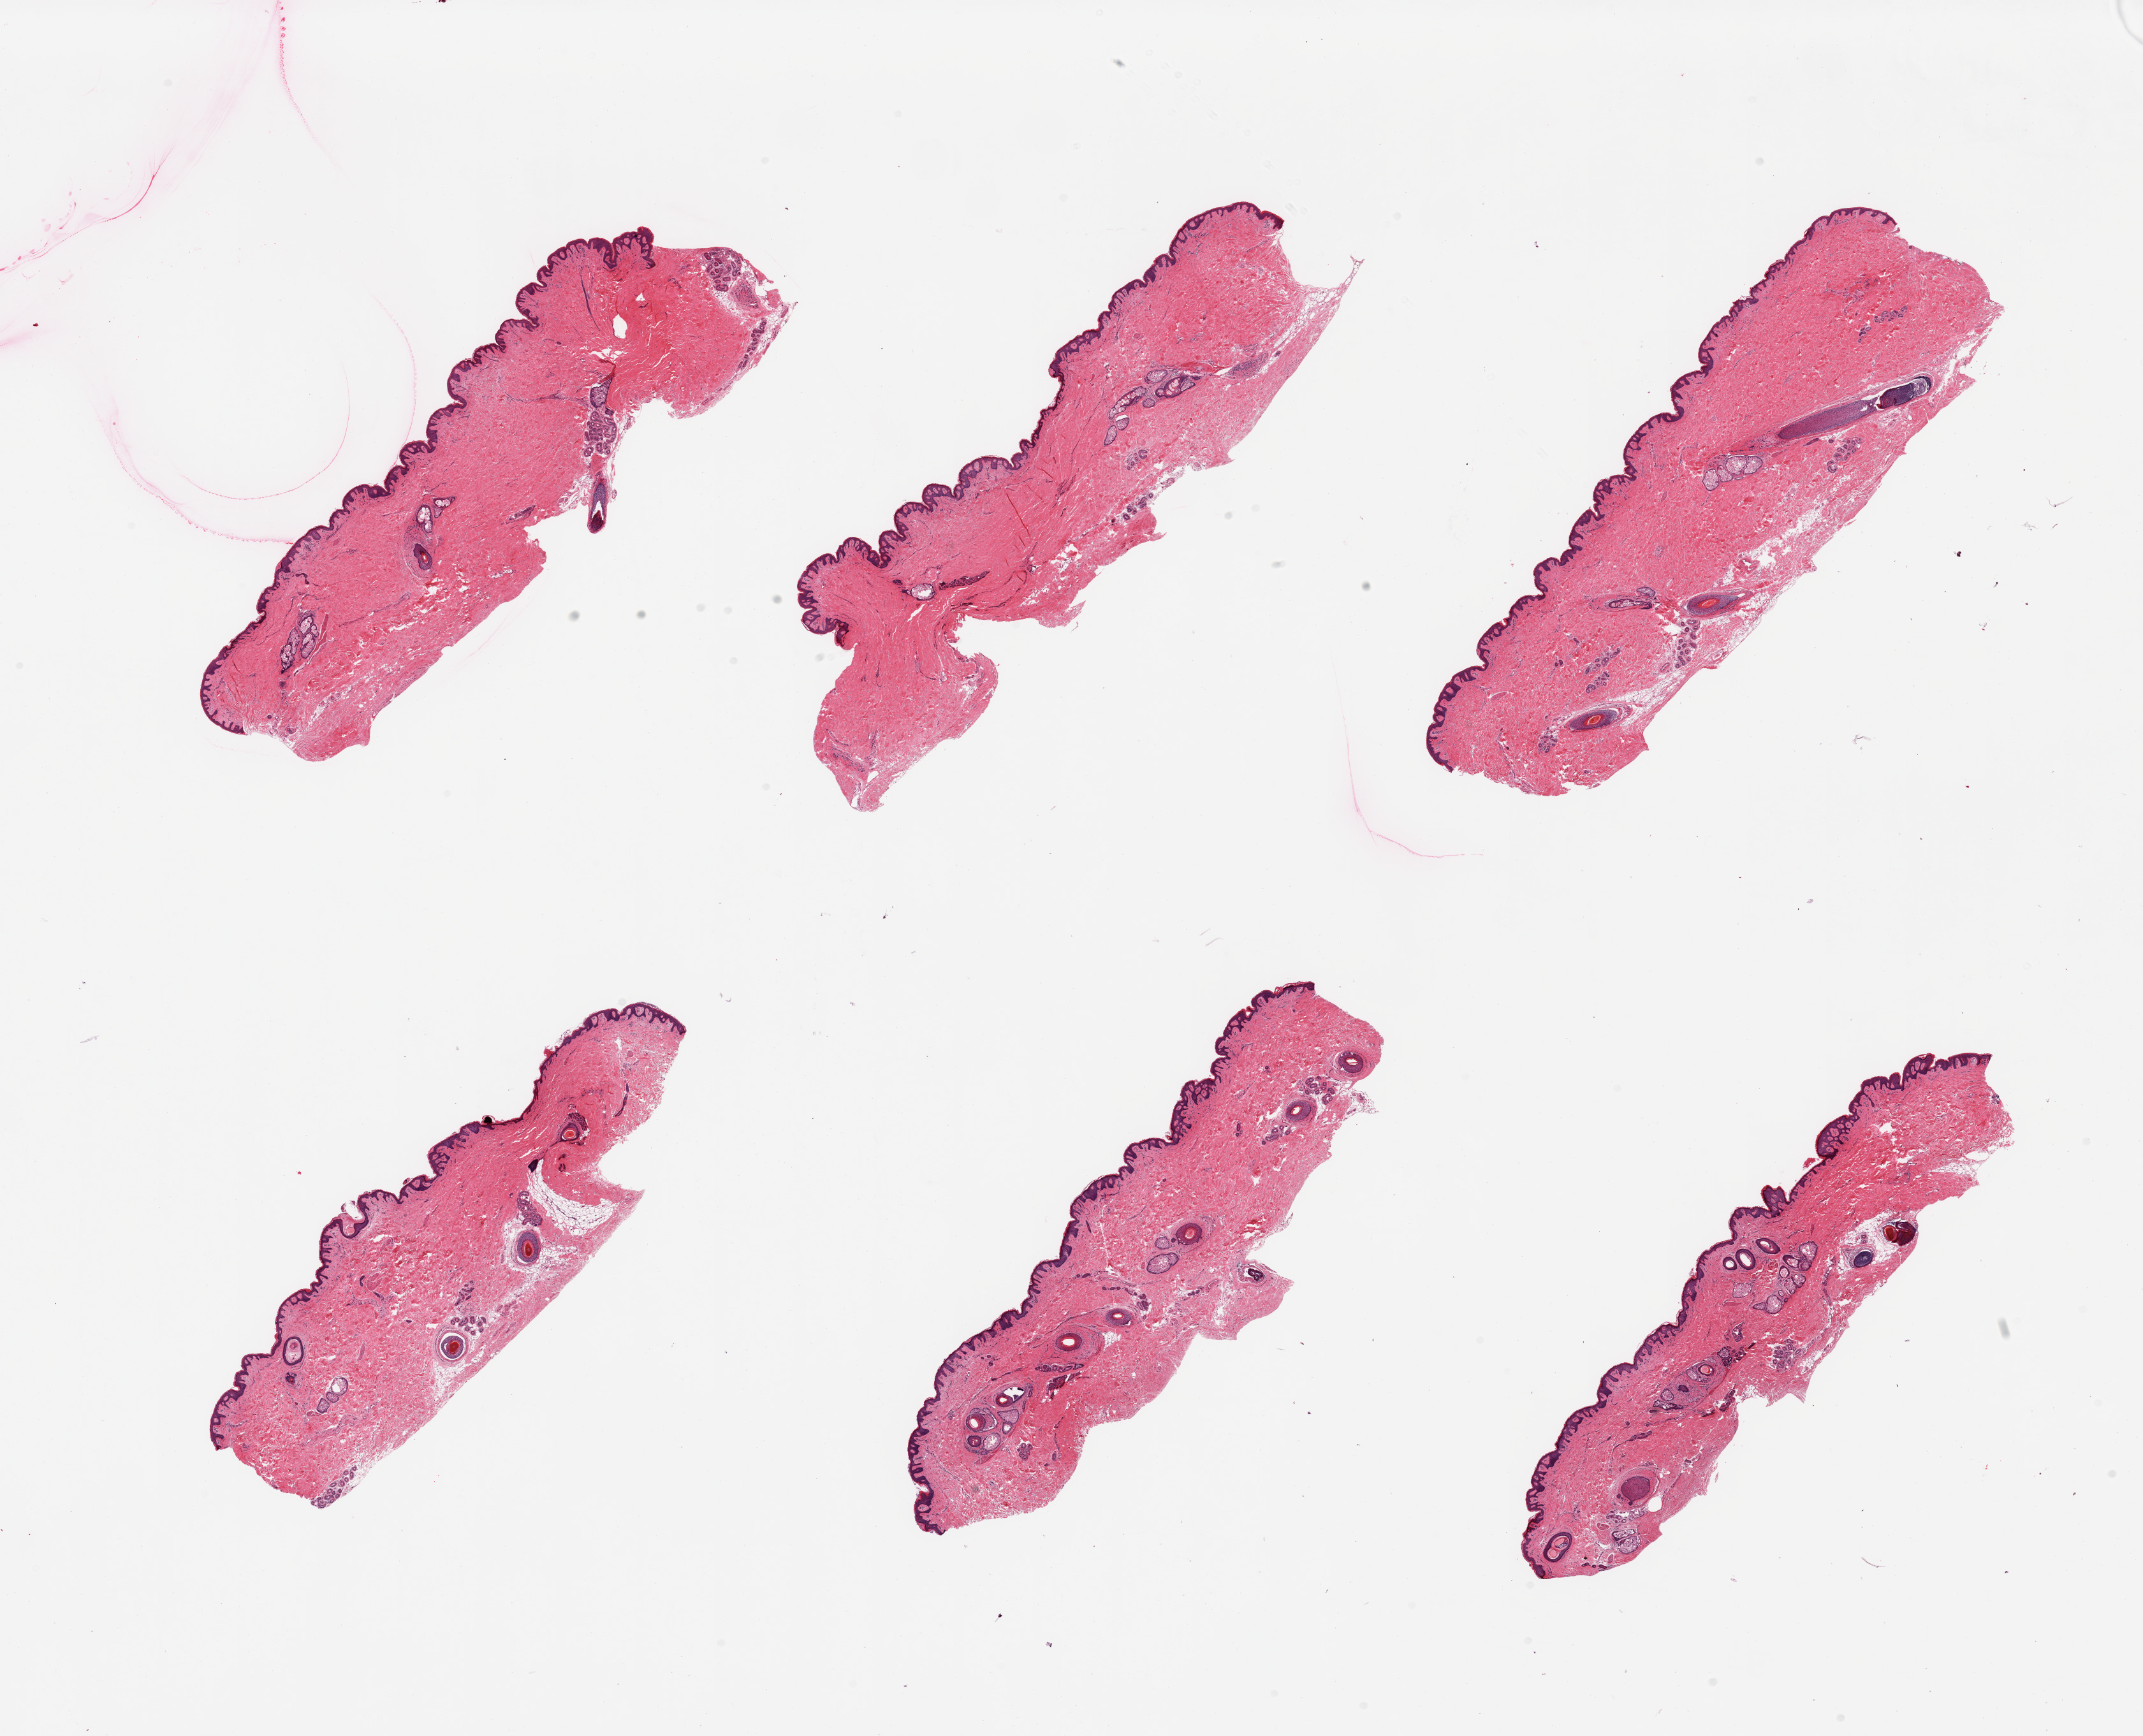
Whole-slide image, hematoxylin and eosin (H&E) stain — whole scanned area (about 26.6 x 21.5 mm, acquisition: 20x scan) shown as a low-resolution overview. PAXgene-fixed paraffin-embedded (PFPE) section. Target tissue: skin of suprapubic region. Donor tissue sample. Donor sex: male.
Pathologist's review note for this sample: 6 pieces; up to 8 hair follicles per piece.